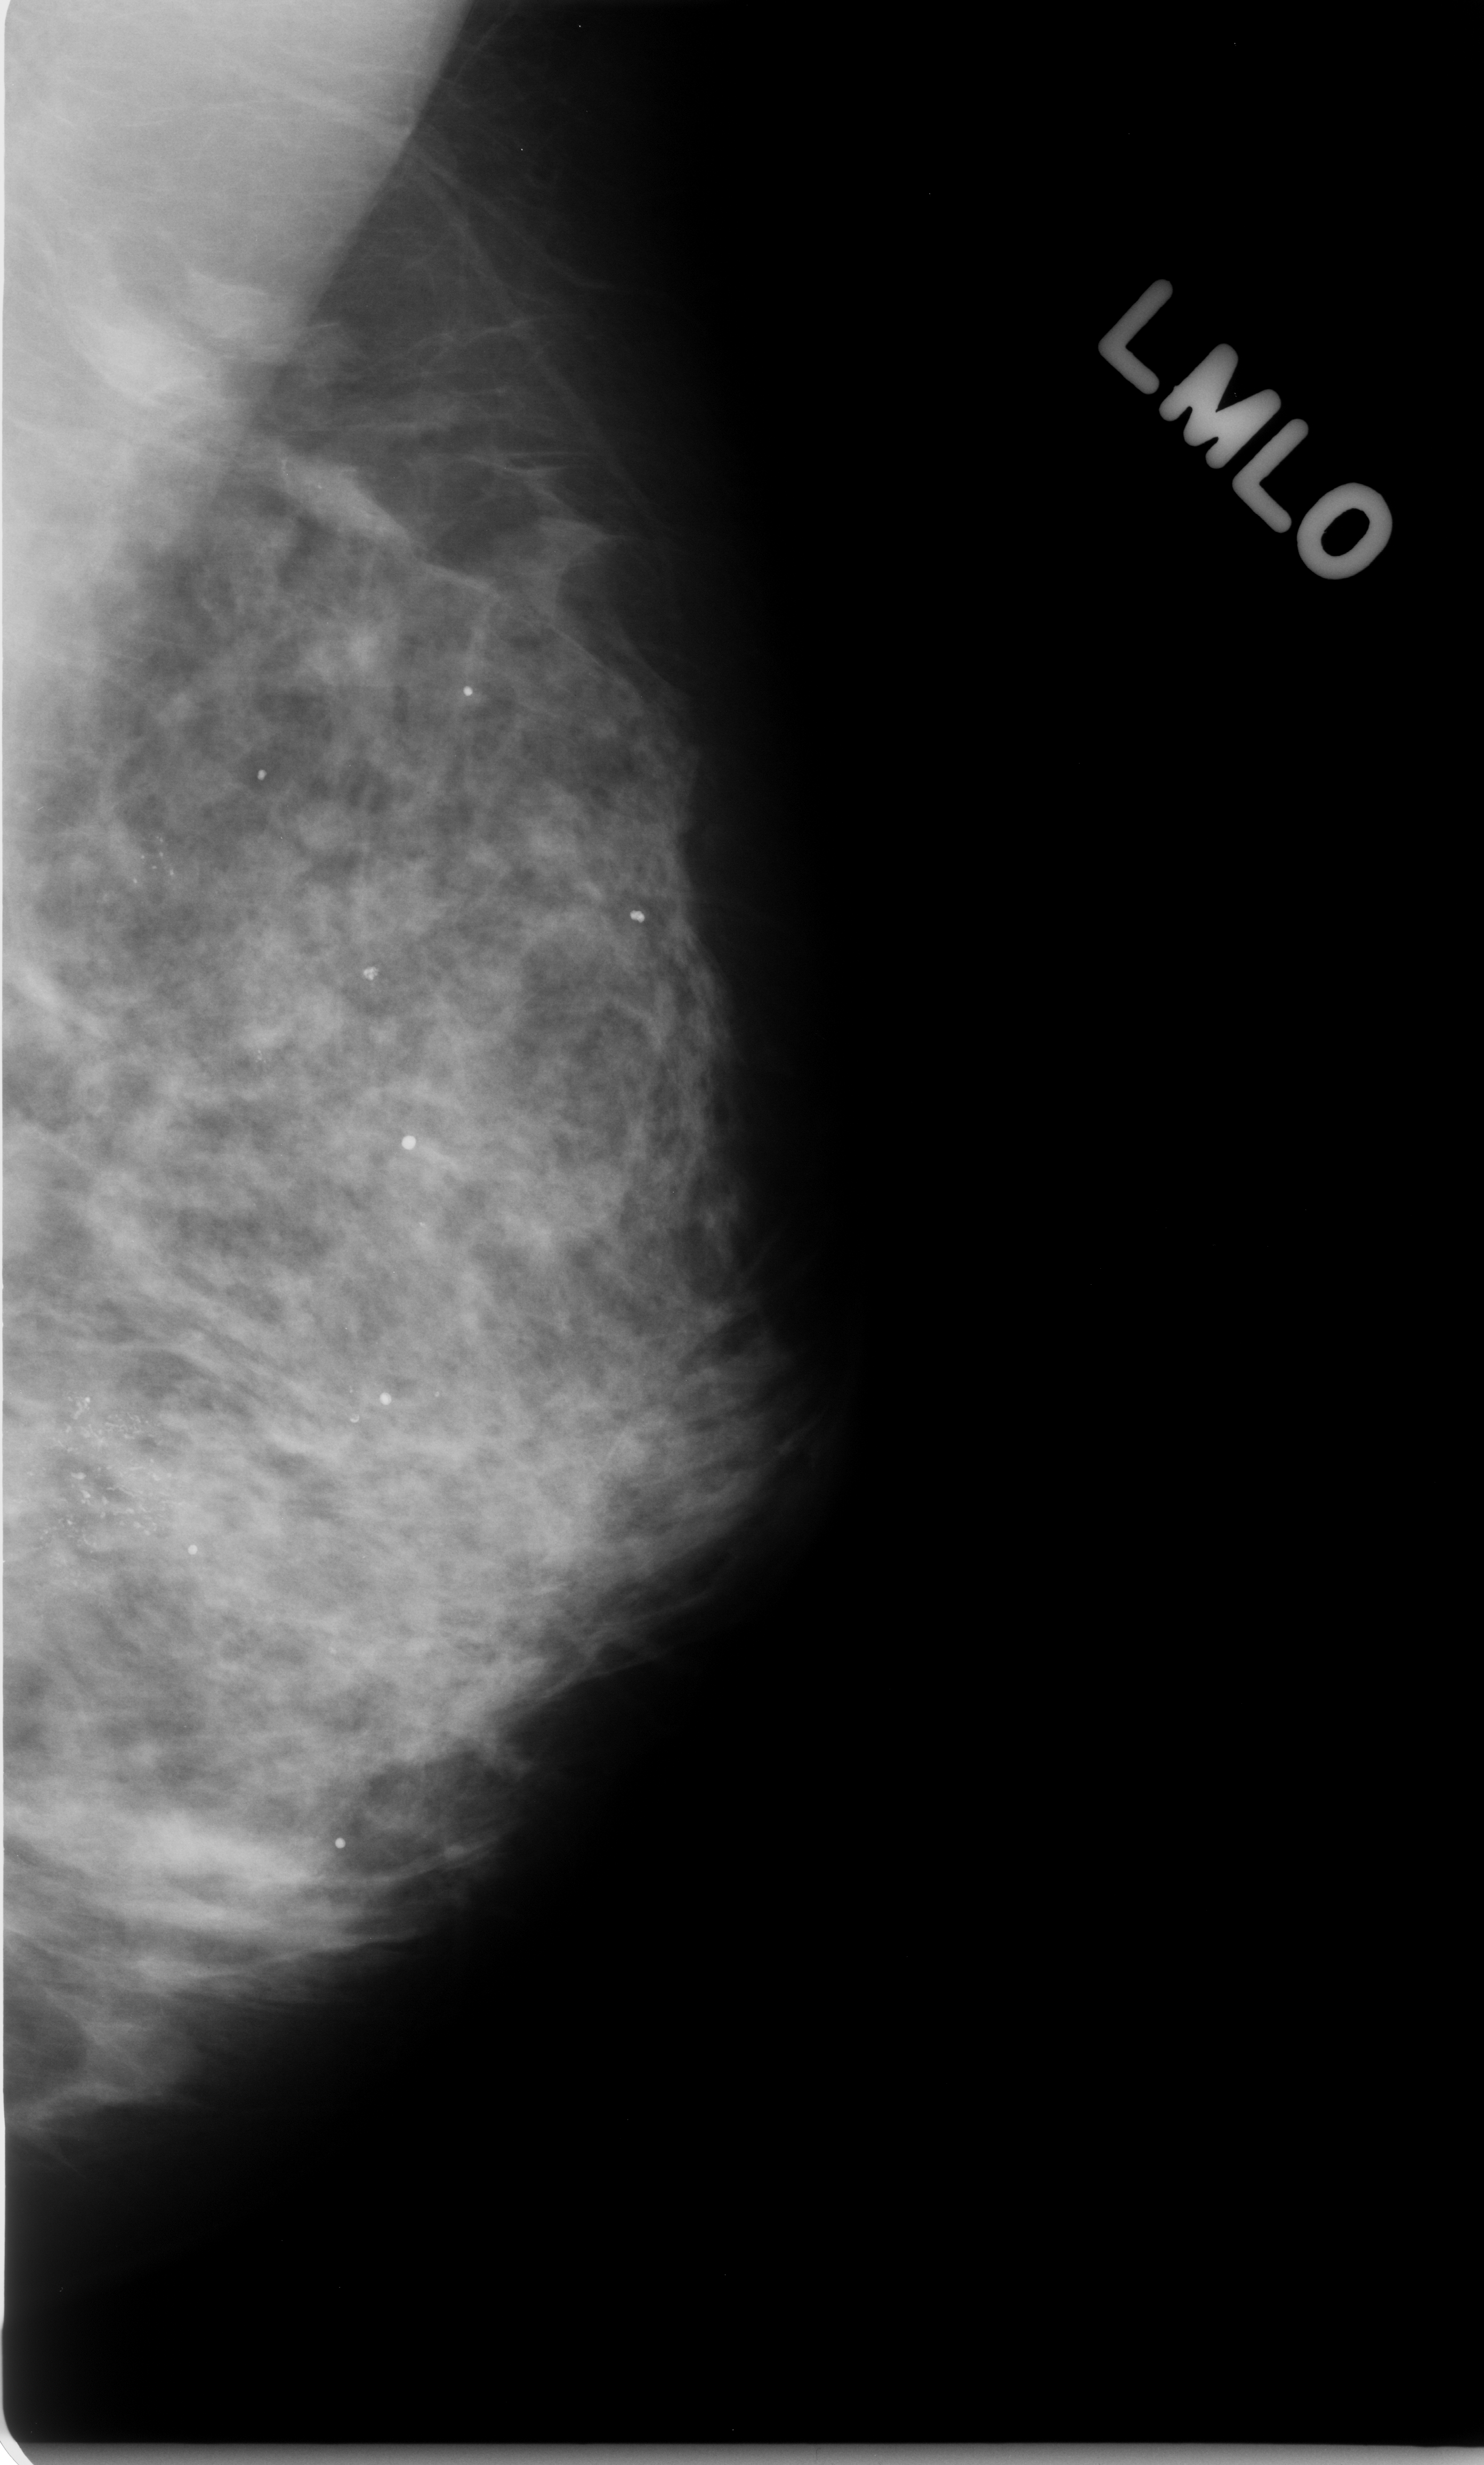
Digitized screen-film mammogram; left breast; MLO view; BI-RADS breast density category 3 (scale 1–4).
Marked findings (only marked abnormalities are described; nothing is implied about the rest of the image): Finding 1 of 2: calcifications, morphology punctate, distribution clustered; BI-RADS assessment category 5; subtlety rating 5 on a 1 (subtle) to 5 (obvious) scale; pathology (as recorded): malignant. Finding 2 of 2: calcifications, morphology fine linear branching, distribution clustered; BI-RADS assessment category 5; subtlety rating 5 on a 1 (subtle) to 5 (obvious) scale; pathology result (as recorded, not read from the image): malignant.